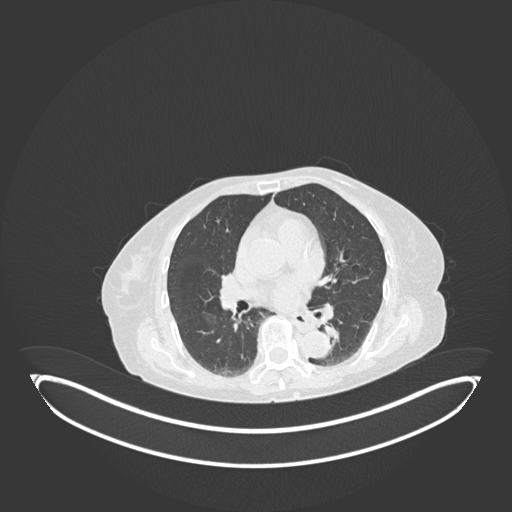
Chest CT, one axial slice. Slice 66 of 189 in the series (ordered by position). 120 kVp. Lung window (W 1500 / L -600 HU). 1 mm slice thickness. 512 × 512 image matrix. Patient: female, 82 years. From the clinical record (not read from this slice): clinical TNM (as recorded): T1b N0 M1.
Outlined on this slice (rectangle marked by the reading radiologist):
- lung tumour (recorded histology: adenocarcinoma): bounding box [x1, y1, x2, y2] px = [320, 321, 346, 346]